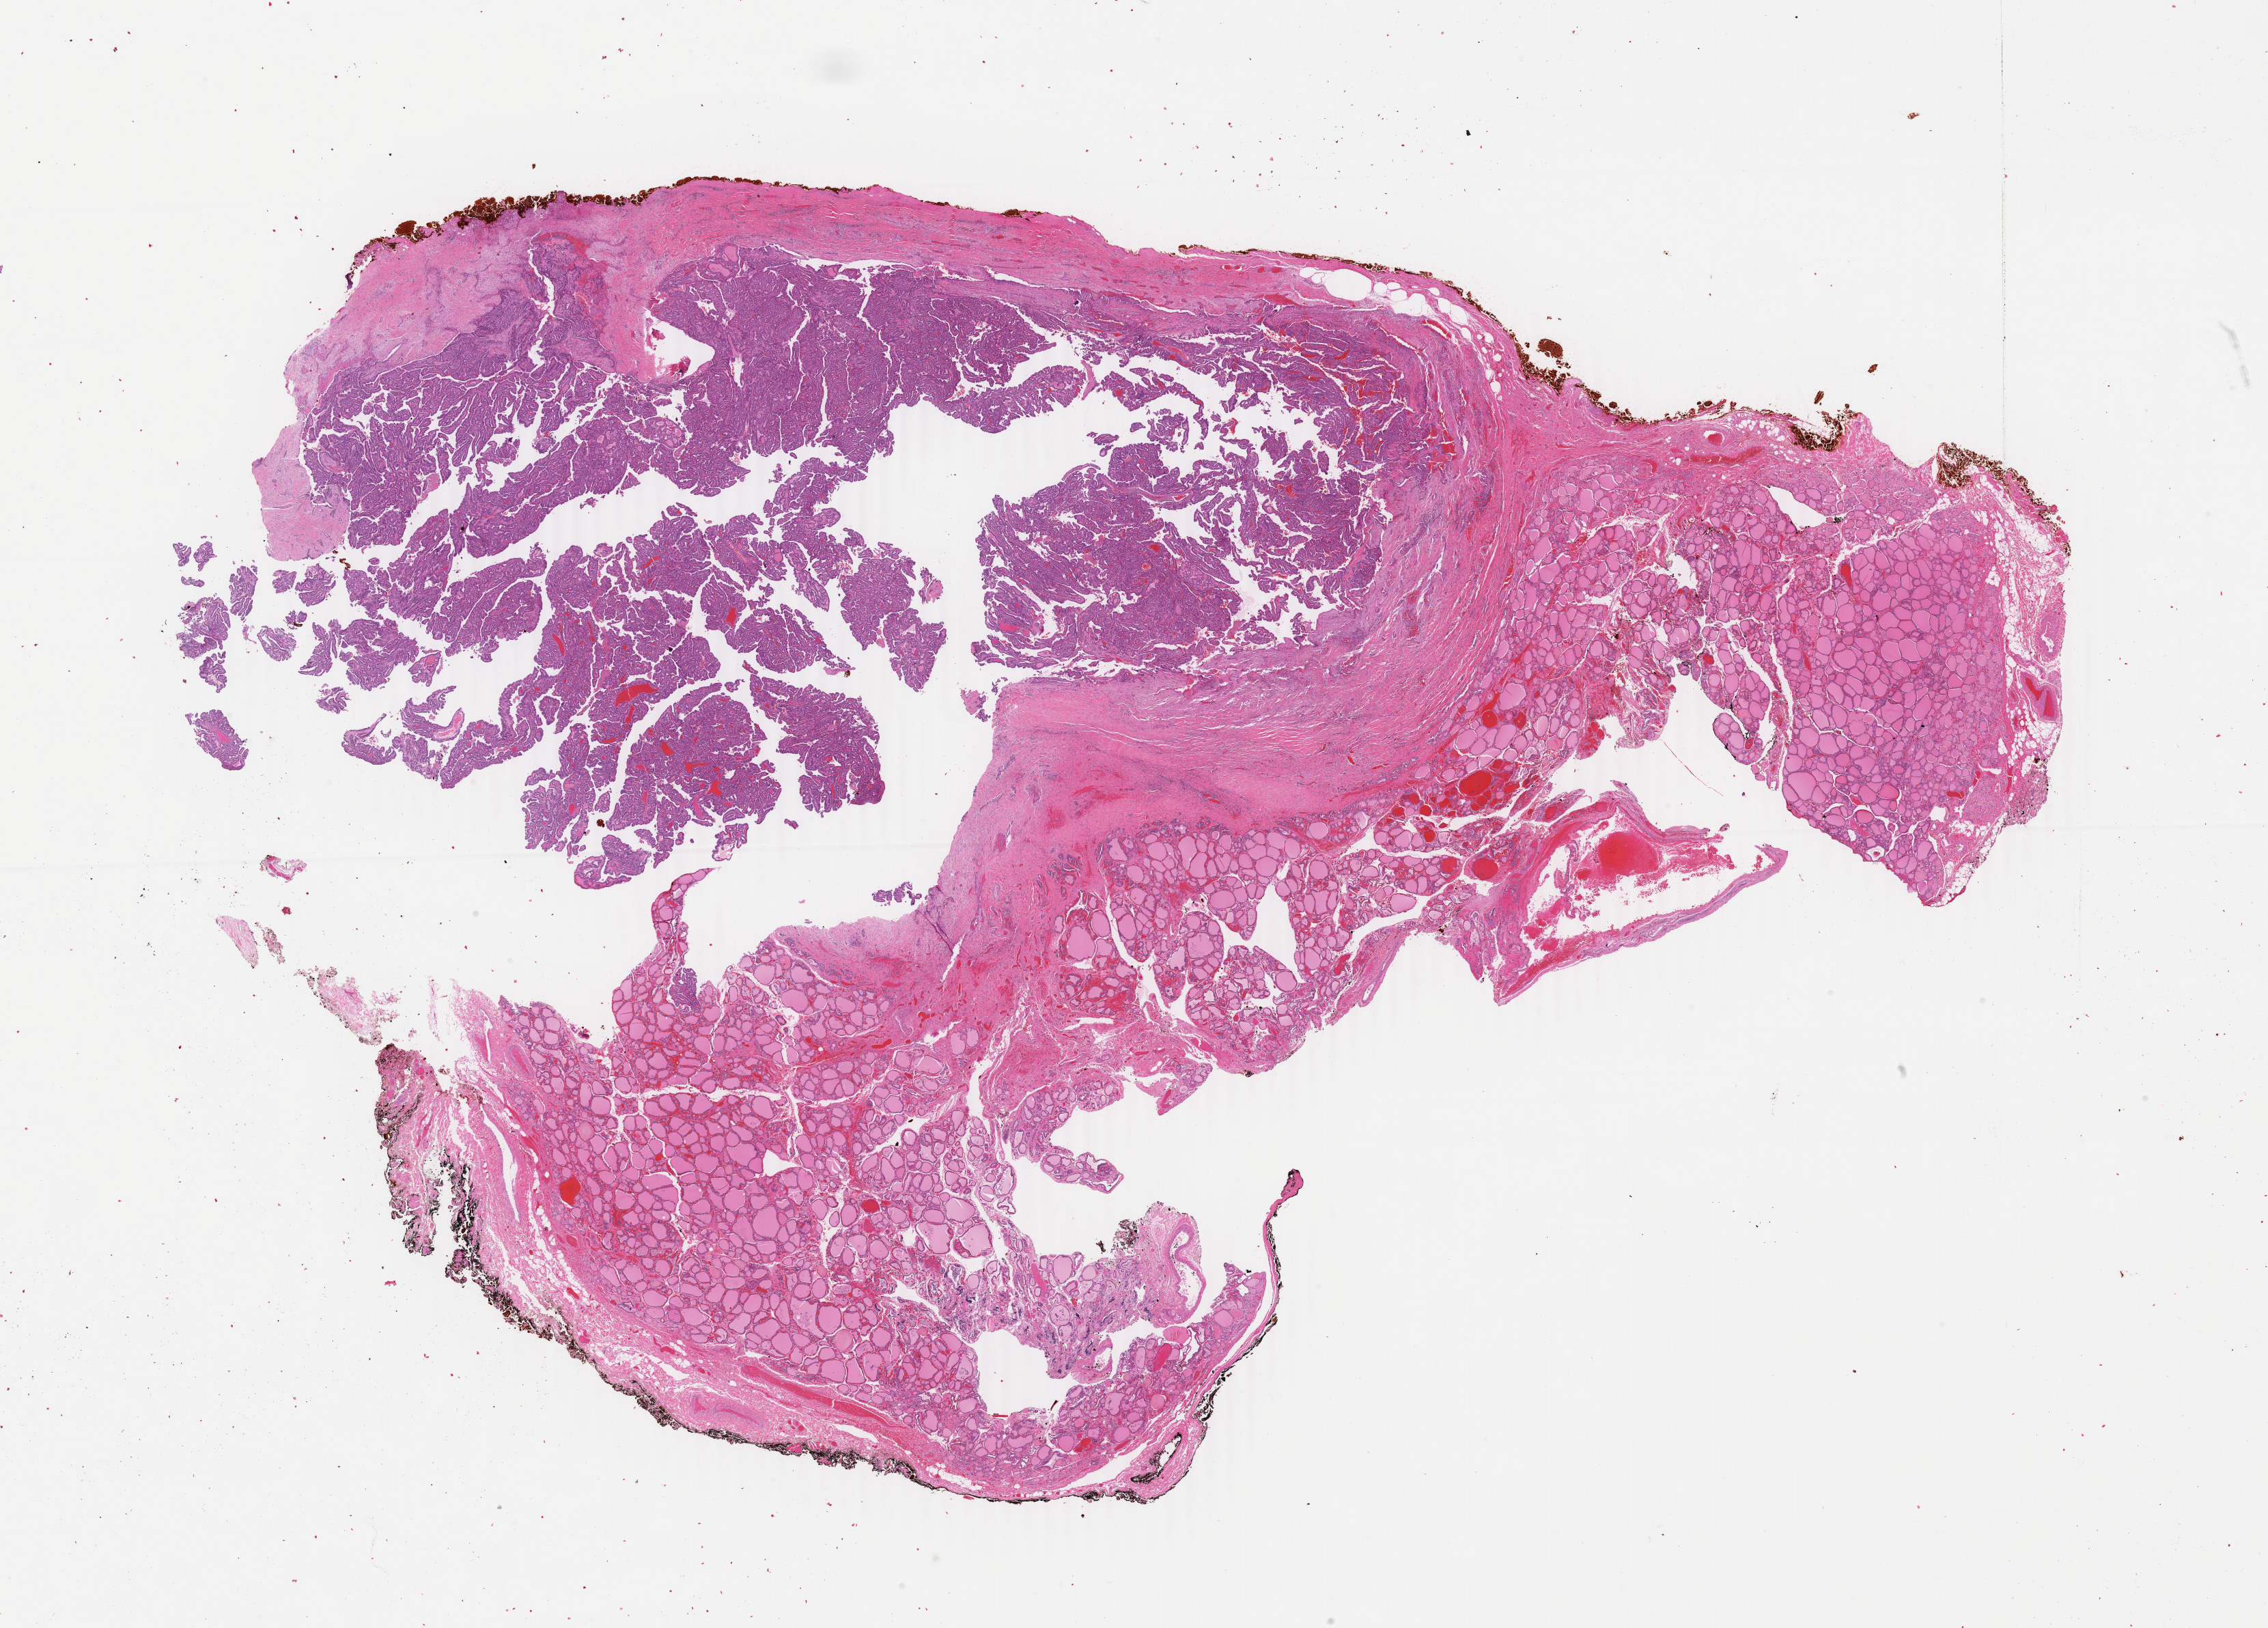
Whole-slide histology image, H&E — a low-resolution overview of the entire scanned area, about 26.4 x 19.0 mm, formalin-fixed paraffin-embedded (FFPE) diagnostic section, primary tumour sample from the thyroid. Female, age 35 years at initial diagnosis.
* AJCC pathologic stage: I
* lymph nodes positive (case pathology): 2 of 5 examined
* TNM: T2 N1a MX
* histologic diagnosis: Papillary adenocarcinoma, NOS (thyroid gland)